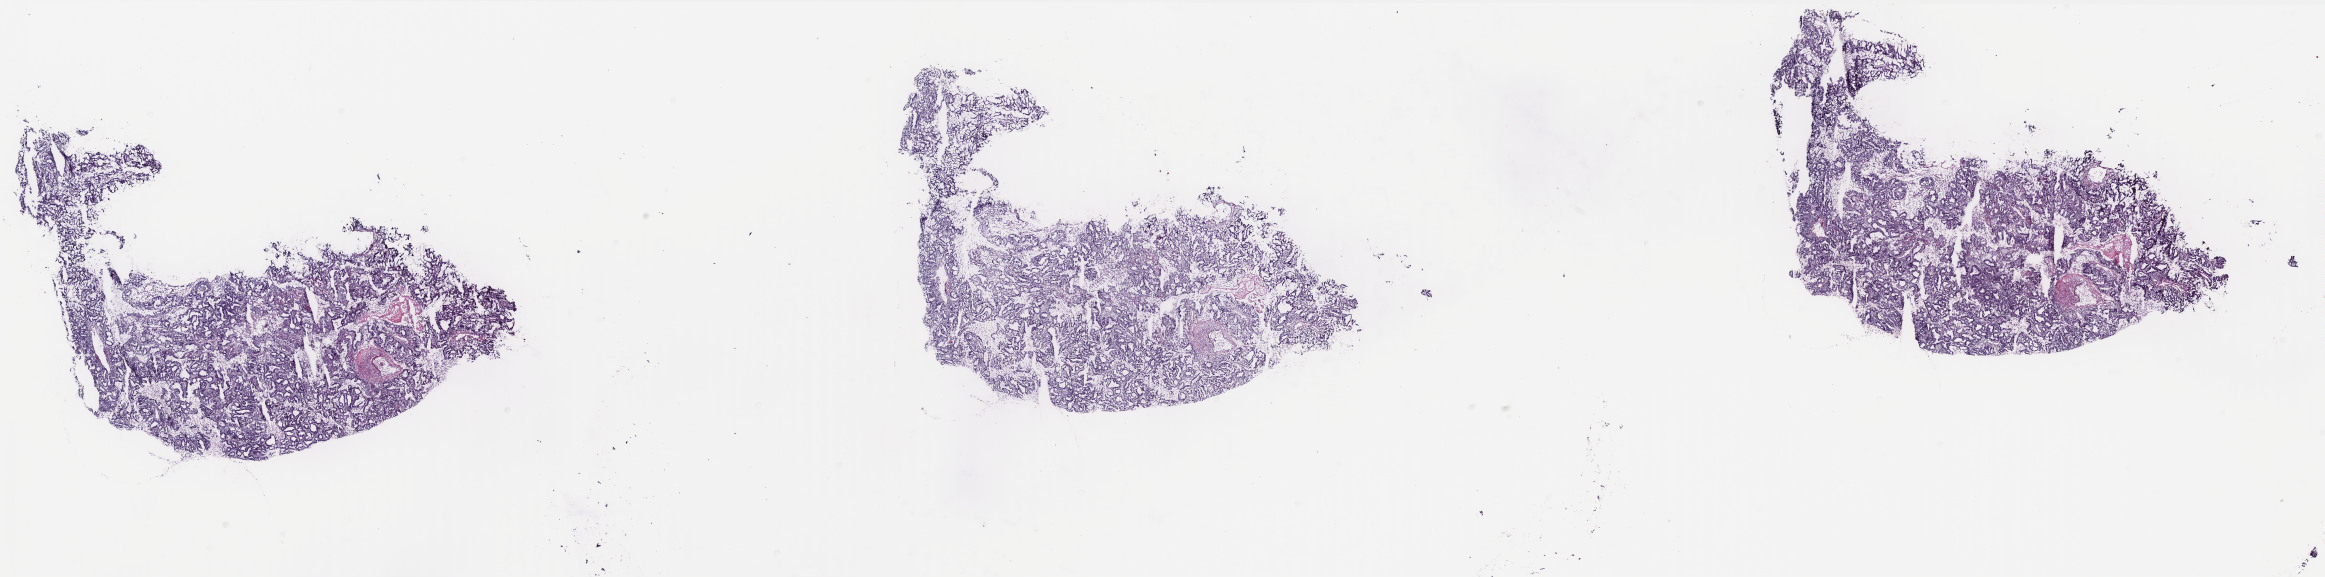
H&E whole-slide image — whole scanned area (about 37.3 x 9.3 mm) shown as a low-resolution overview. Frozen section. Uterus, primary tumour sample. Female patient; age at initial diagnosis 65 years. Histologic grade: G1 (well differentiated). Pathologist review of this section (percent, as recorded): tumour cells 100%, tumour nuclei 80%, normal cells 0%, stromal cells 0%, necrosis 0%. Inflammatory infiltration, as recorded: lymphocyte infiltration 1%, monocyte infiltration 0%, neutrophil infiltration 0%.
FIGO stage: IB. Diagnosis: Endometrioid adenocarcinoma, NOS (endometrium).